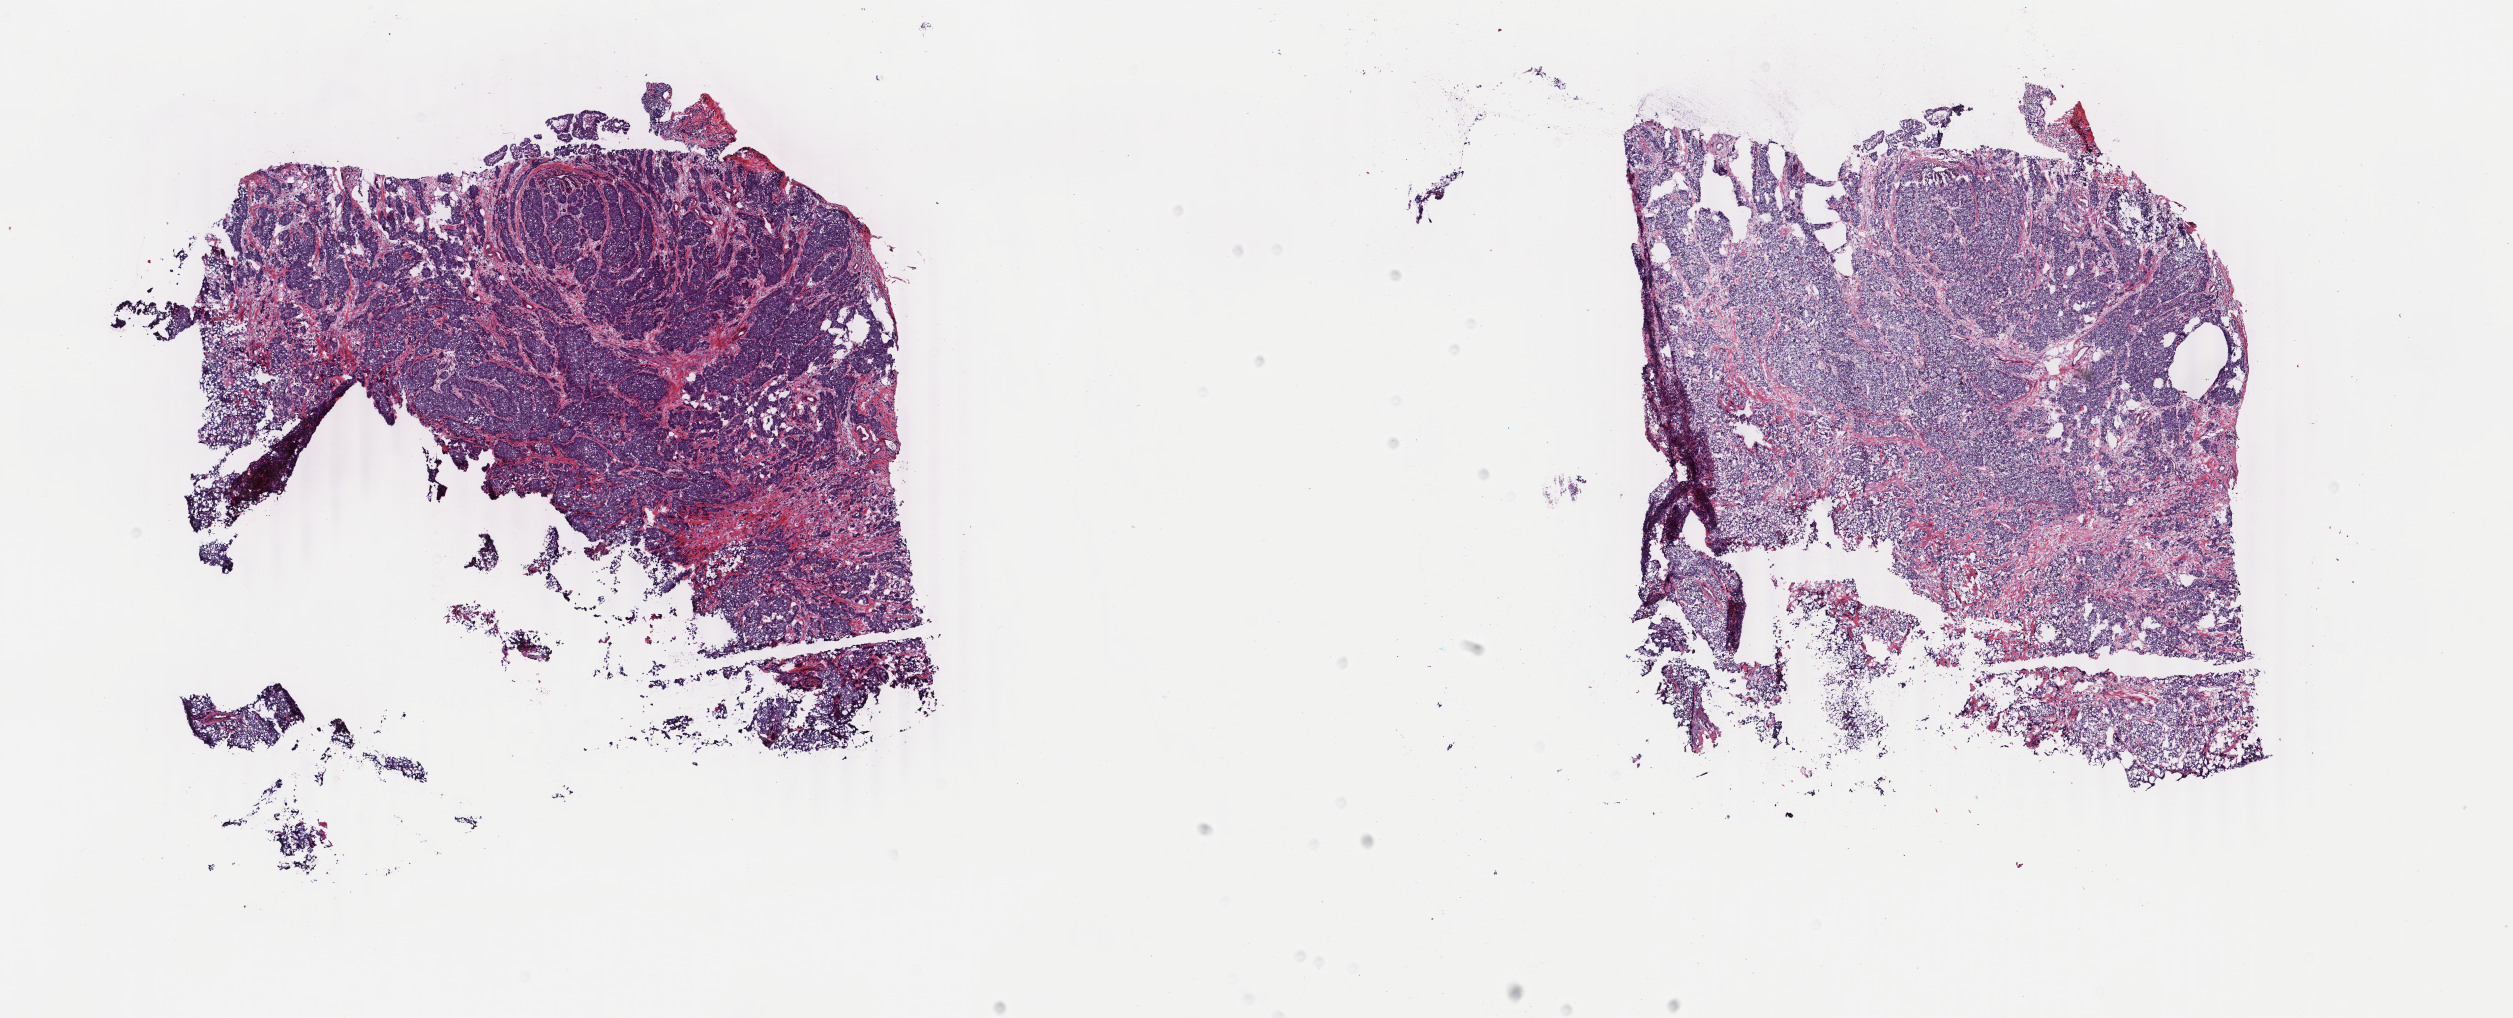
H&E whole-slide image, whole scanned area (about 20.0 x 8.1 mm, acquisition: 40x scan) shown as a low-resolution overview, frozen section from the top of the tissue portion, breast, primary tumour sample. Female, age 71 years at initial diagnosis. Composition of this section per pathologist review: tumour cells 90%, tumour nuclei 90%, normal cells 0%, stromal cells 10%, necrosis 0%. Inflammatory infiltration, as recorded: lymphocyte infiltration 1%, monocyte infiltration 0%, neutrophil infiltration 0%.
Lymph nodes positive (case pathology): 3 of 11 examined. Pathologic diagnosis: Infiltrating duct mixed with other types of carcinoma. TNM: T2 N1 M0. AJCC pathologic stage: IIB.